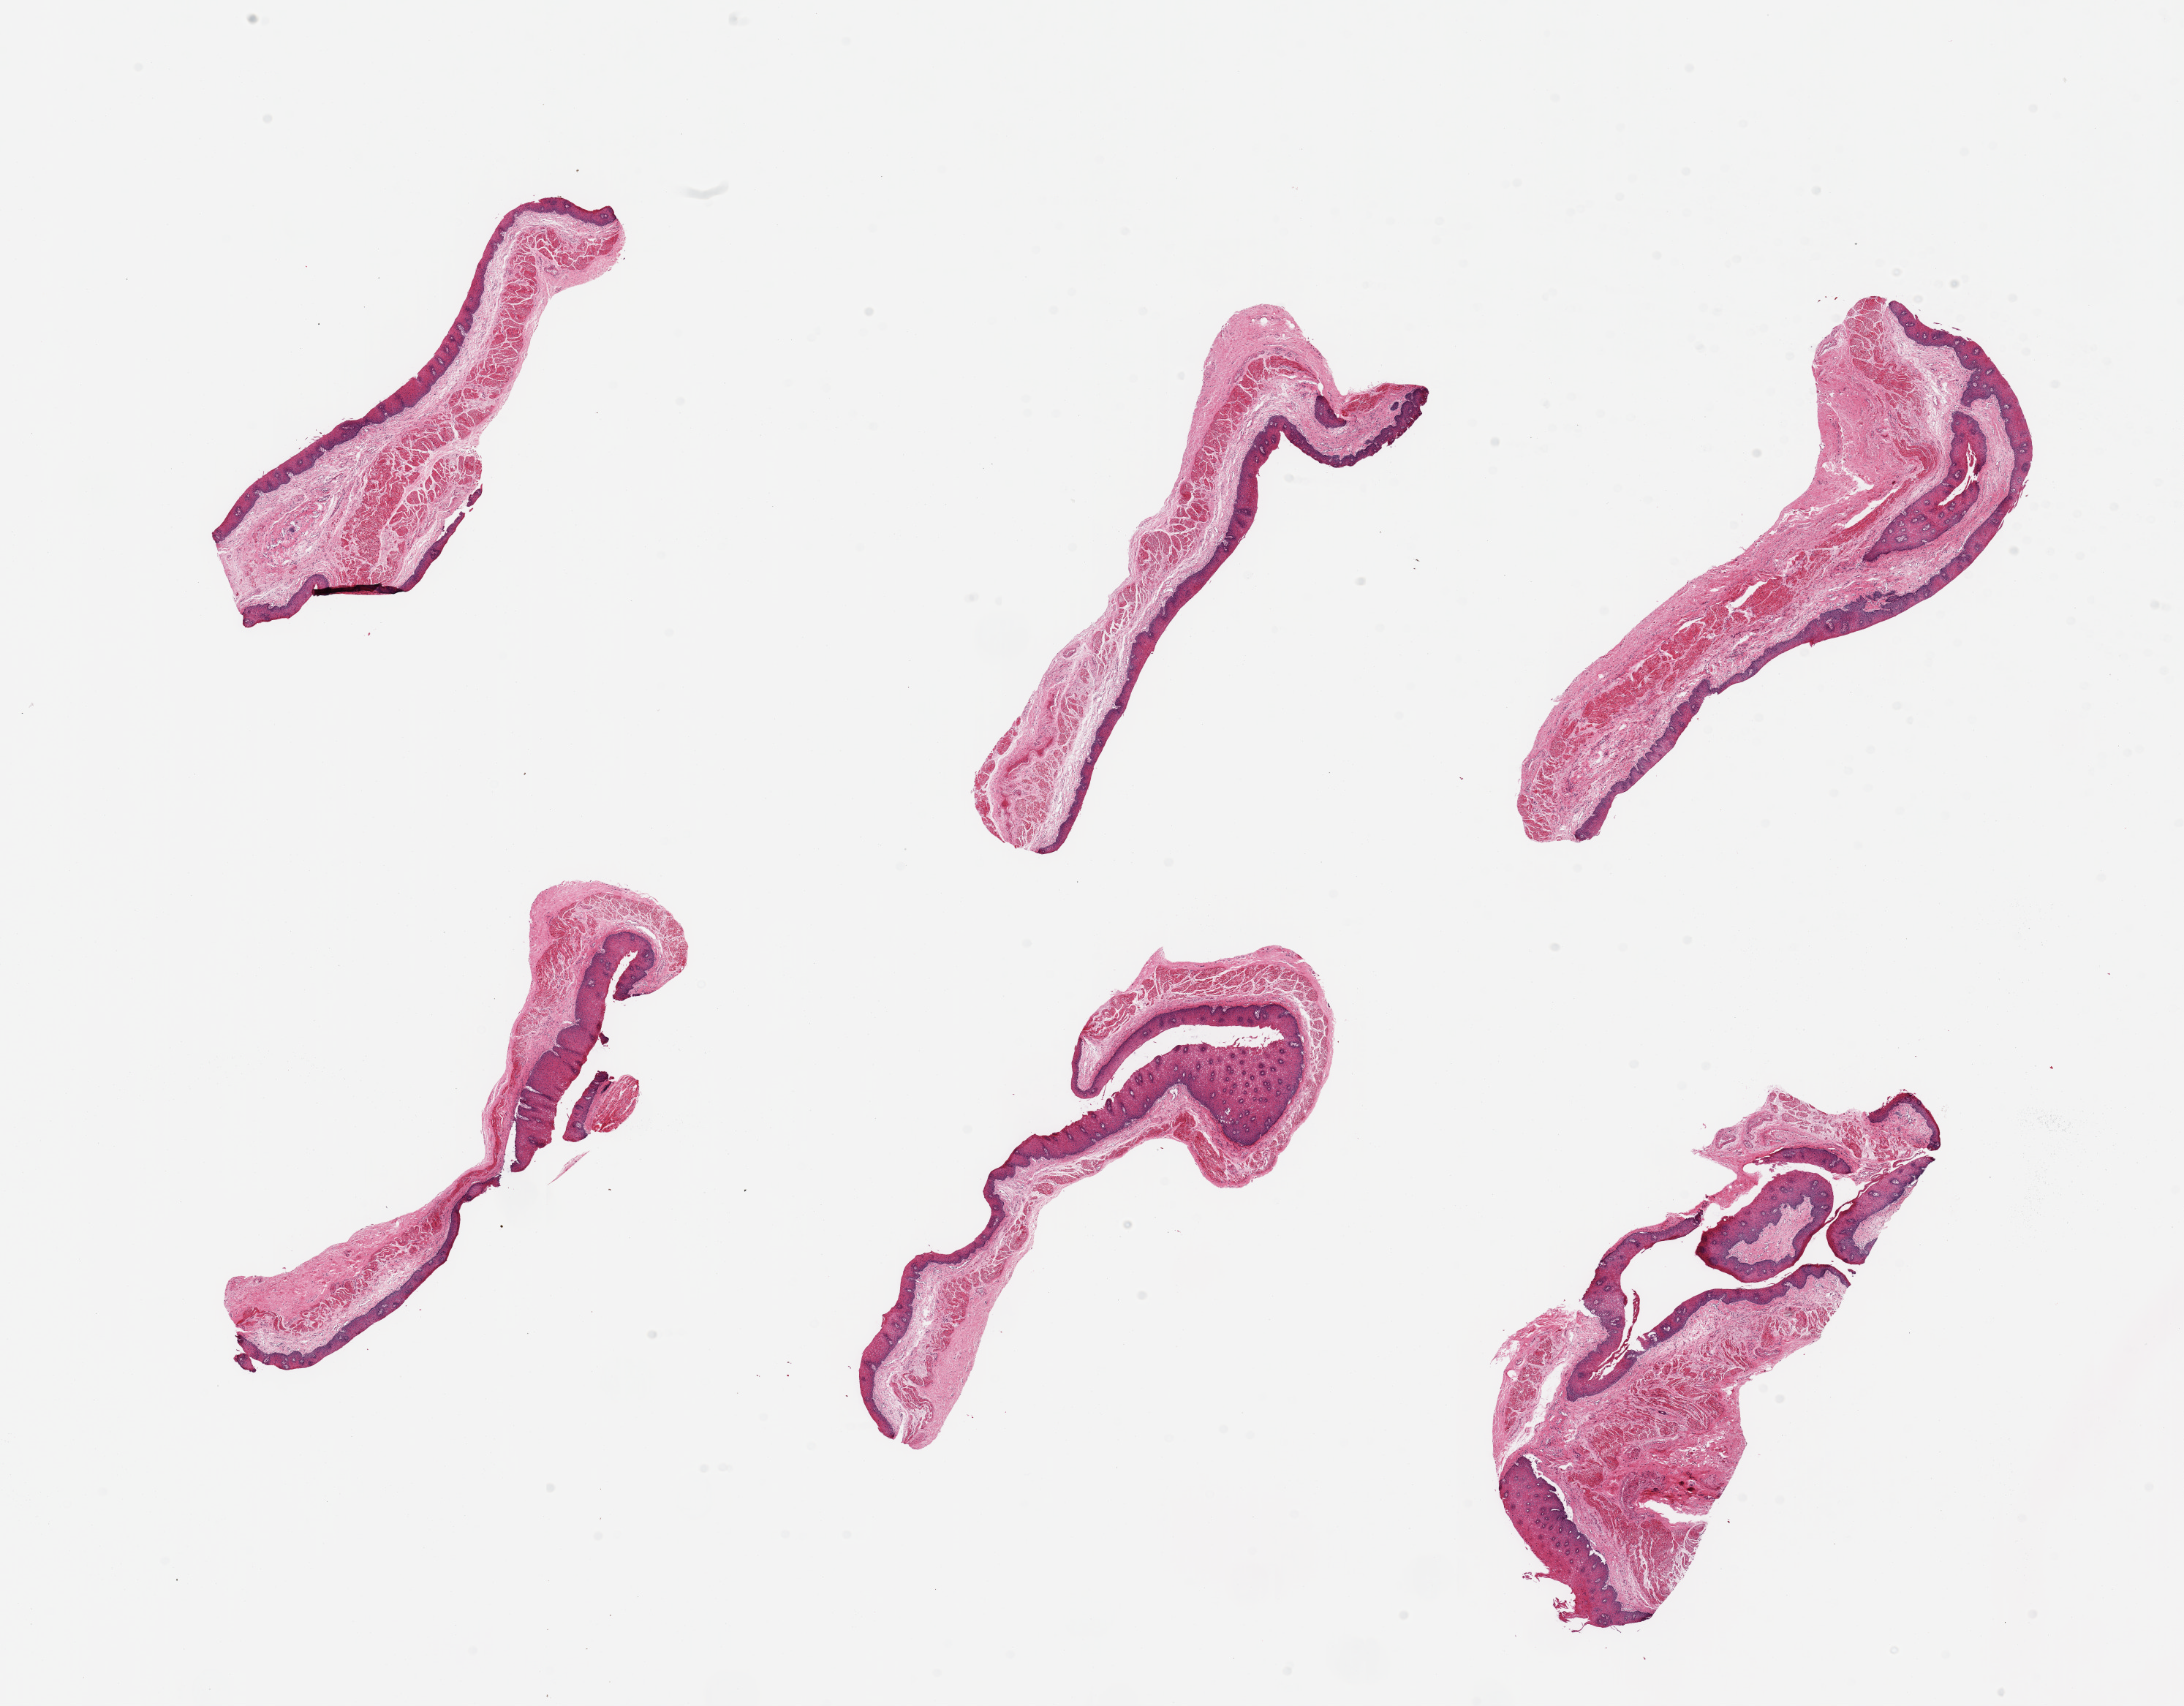
Whole-slide image, haematoxylin and eosin stain, a low-resolution overview of the entire scanned area, about 23.6 x 18.5 mm (acquisition: 20x scan). PAXgene-fixed paraffin-embedded (PFPE) section. Target tissue: esophageal mucous membrane. Tissue donor sample.
Review note (as recorded): 6 pieces.